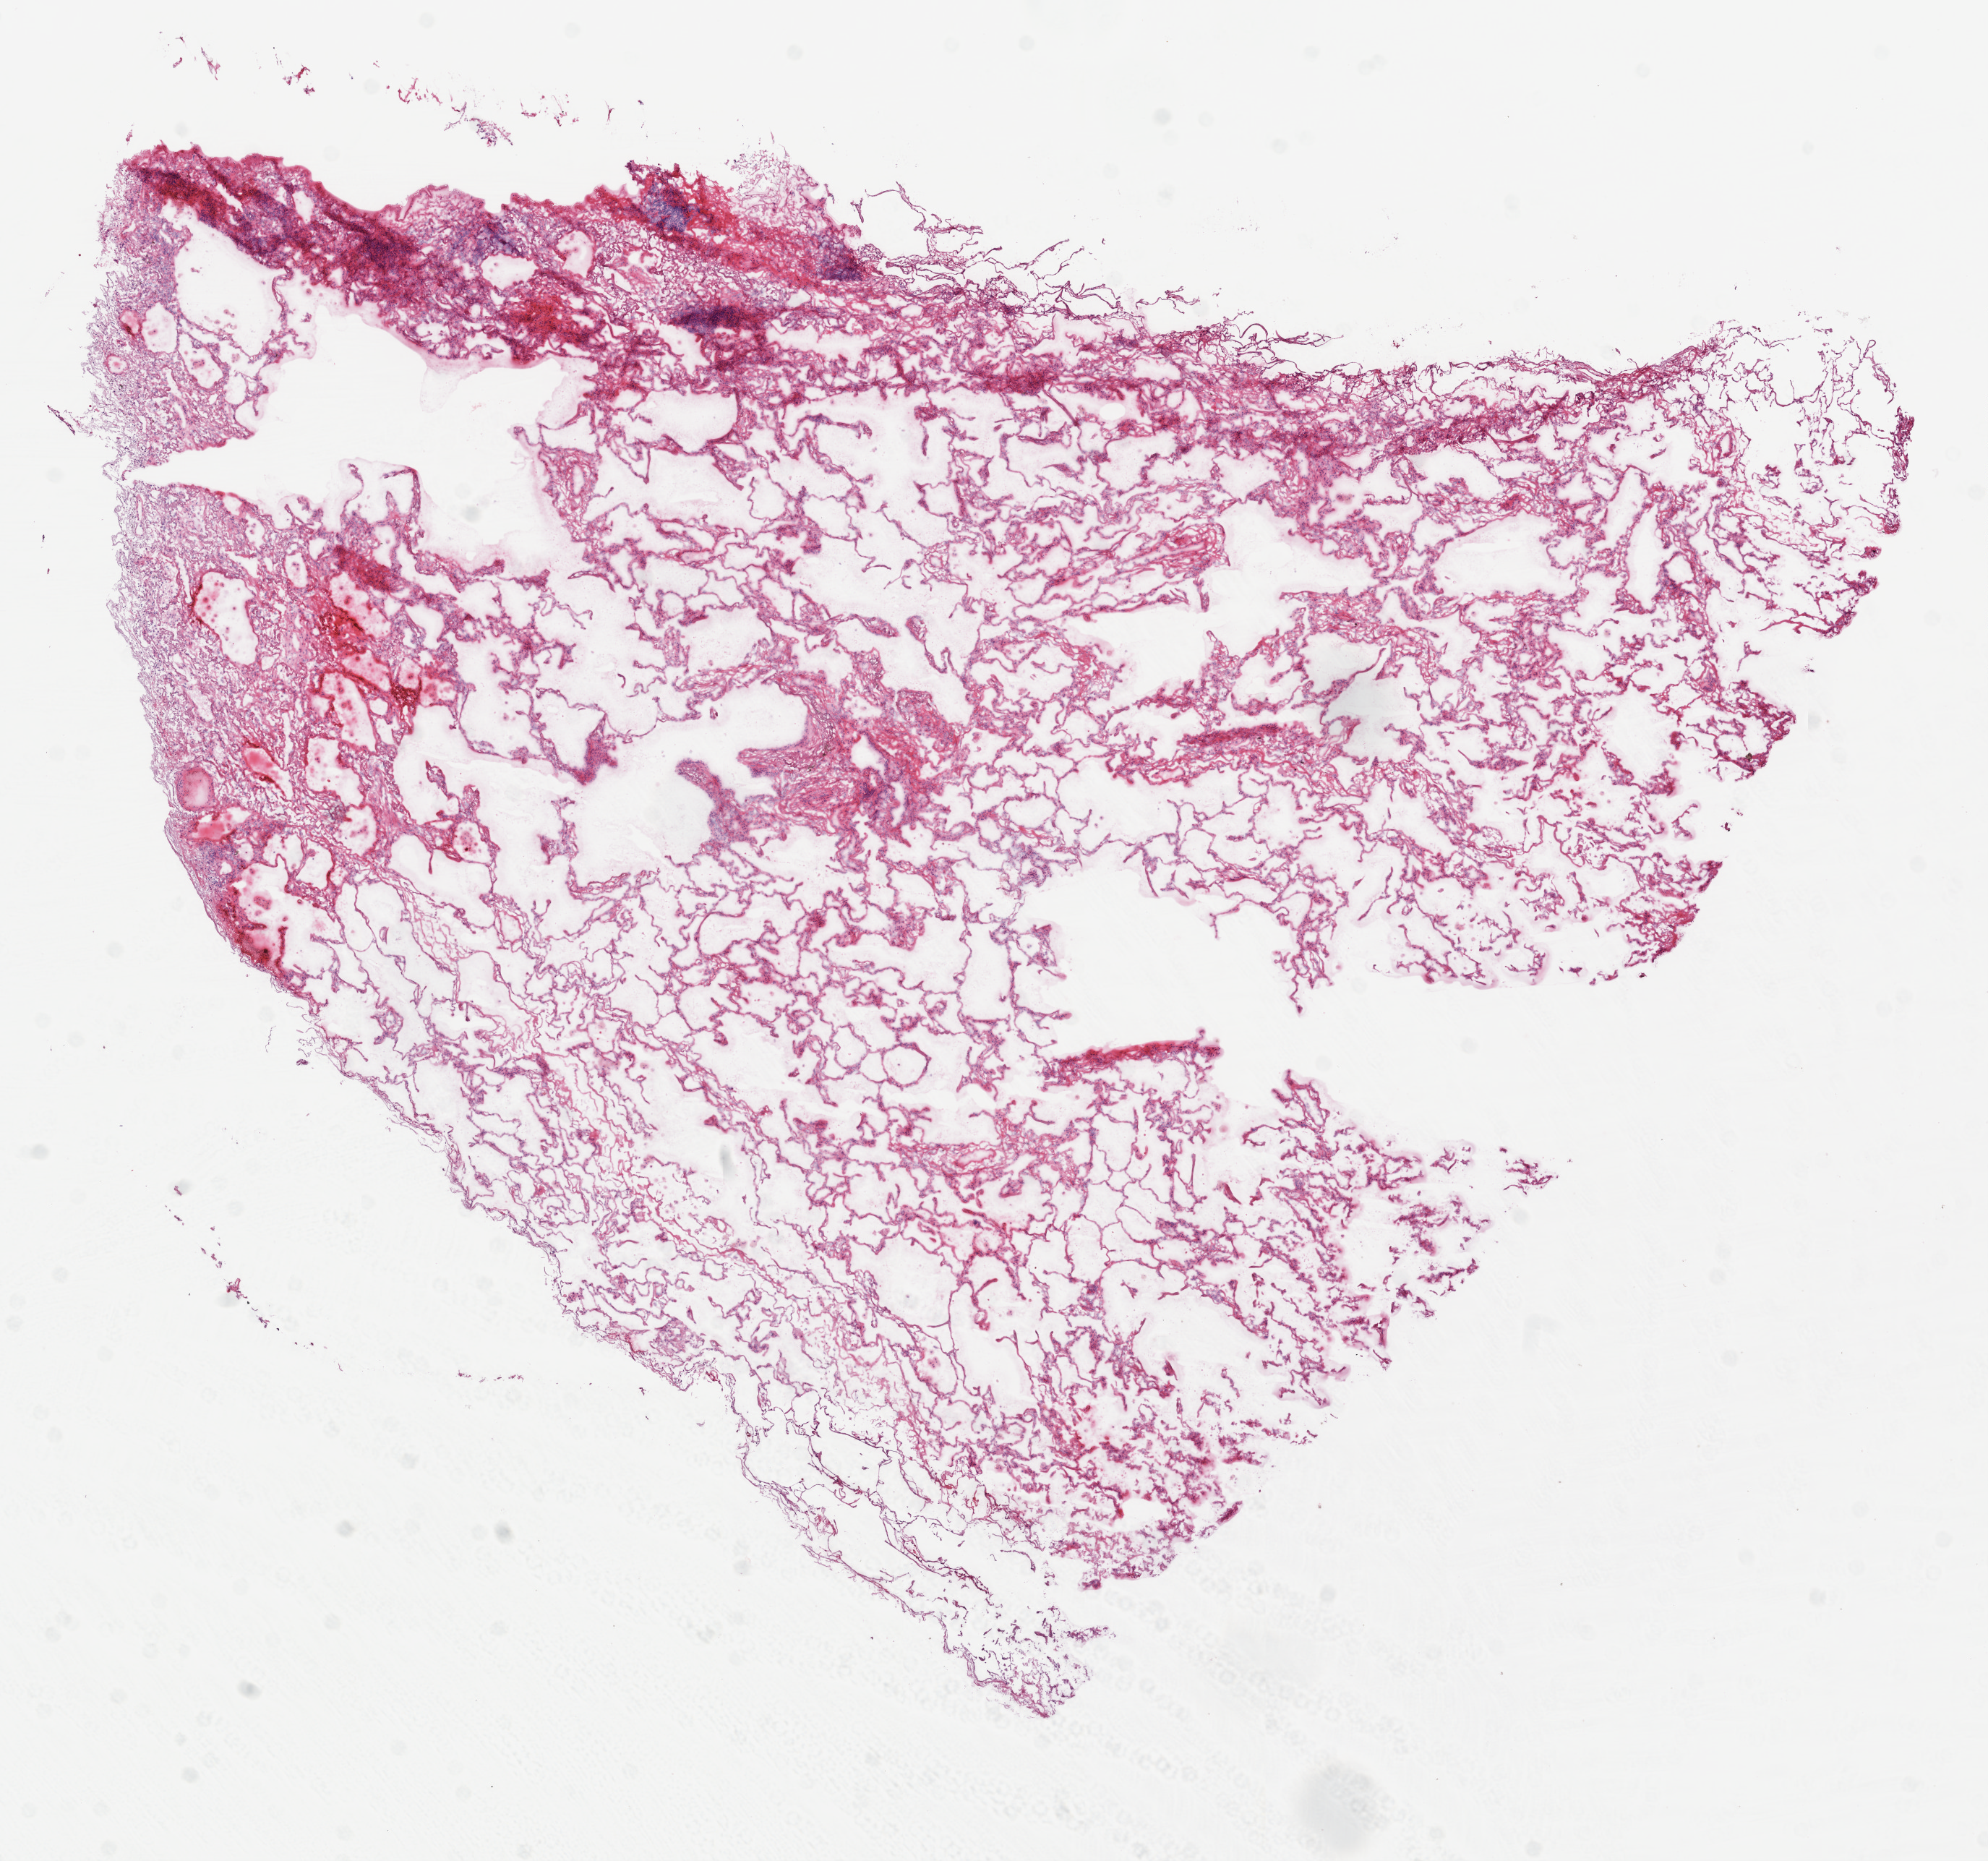
H&E-stained whole-slide image — low-resolution overview of the scanned area, about 11.0 x 10.3 mm, frozen section, lung, solid tissue normal (non-tumour tissue) sample. Patient: female, age at initial diagnosis 66 years.
* this section: solid tissue normal sample (biorepository sample class)
* patient diagnosis: Squamous cell carcinoma, NOS (upper lobe, lung)